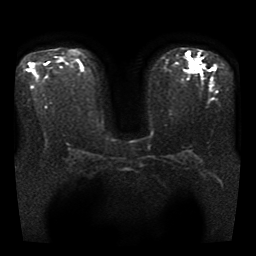
Breast MRI, one axial slice. Slice 24 of 40 in the series (ordered by position). Diffusion-weighted series; image 2 of 4 stored at this slice position (different b-values; order by instance number). 1.5 T. 5 mm slice thickness. 256 × 256 image matrix, field of view 330 × 330 mm. Female patient.
Structures marked on this image (outlined manually by an expert reader):
- tumour on diffusion-weighted imaging: box from (x=189, y=60) to (x=200, y=74) px